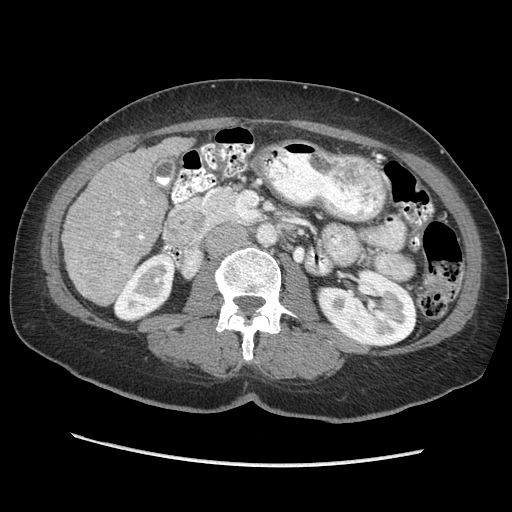
Contrast-enhanced abdominal CT (liver protocol), one axial slice. Slice 104 of 170 in the series (ordered by position). Reconstruction kernel STANDARD. 140 kVp. Soft-tissue window (W 400 / L 40 HU). 2.5 mm slice thickness. 512 × 512 image matrix, field of view 360 × 360 mm. Case-level facts recorded for this patient, not image findings: diagnosis: hepatocellular carcinoma (patient treated with transarterial chemoembolisation; whether this scan precedes or follows treatment is not stated here); TNM stage (as recorded): Stage-II; Child-Pugh class: A; tumour differentiation: no biopsy.
Outlined on this slice (semi-automatically segmented with operator editing):
- liver parenchyma outside the tumour (the mass and vessels are separate outlines, so this box may not span the whole liver): bounding box <62,138,192,304> (left, top, right, bottom; pixels)
- liver vessels: <114,199,145,272>